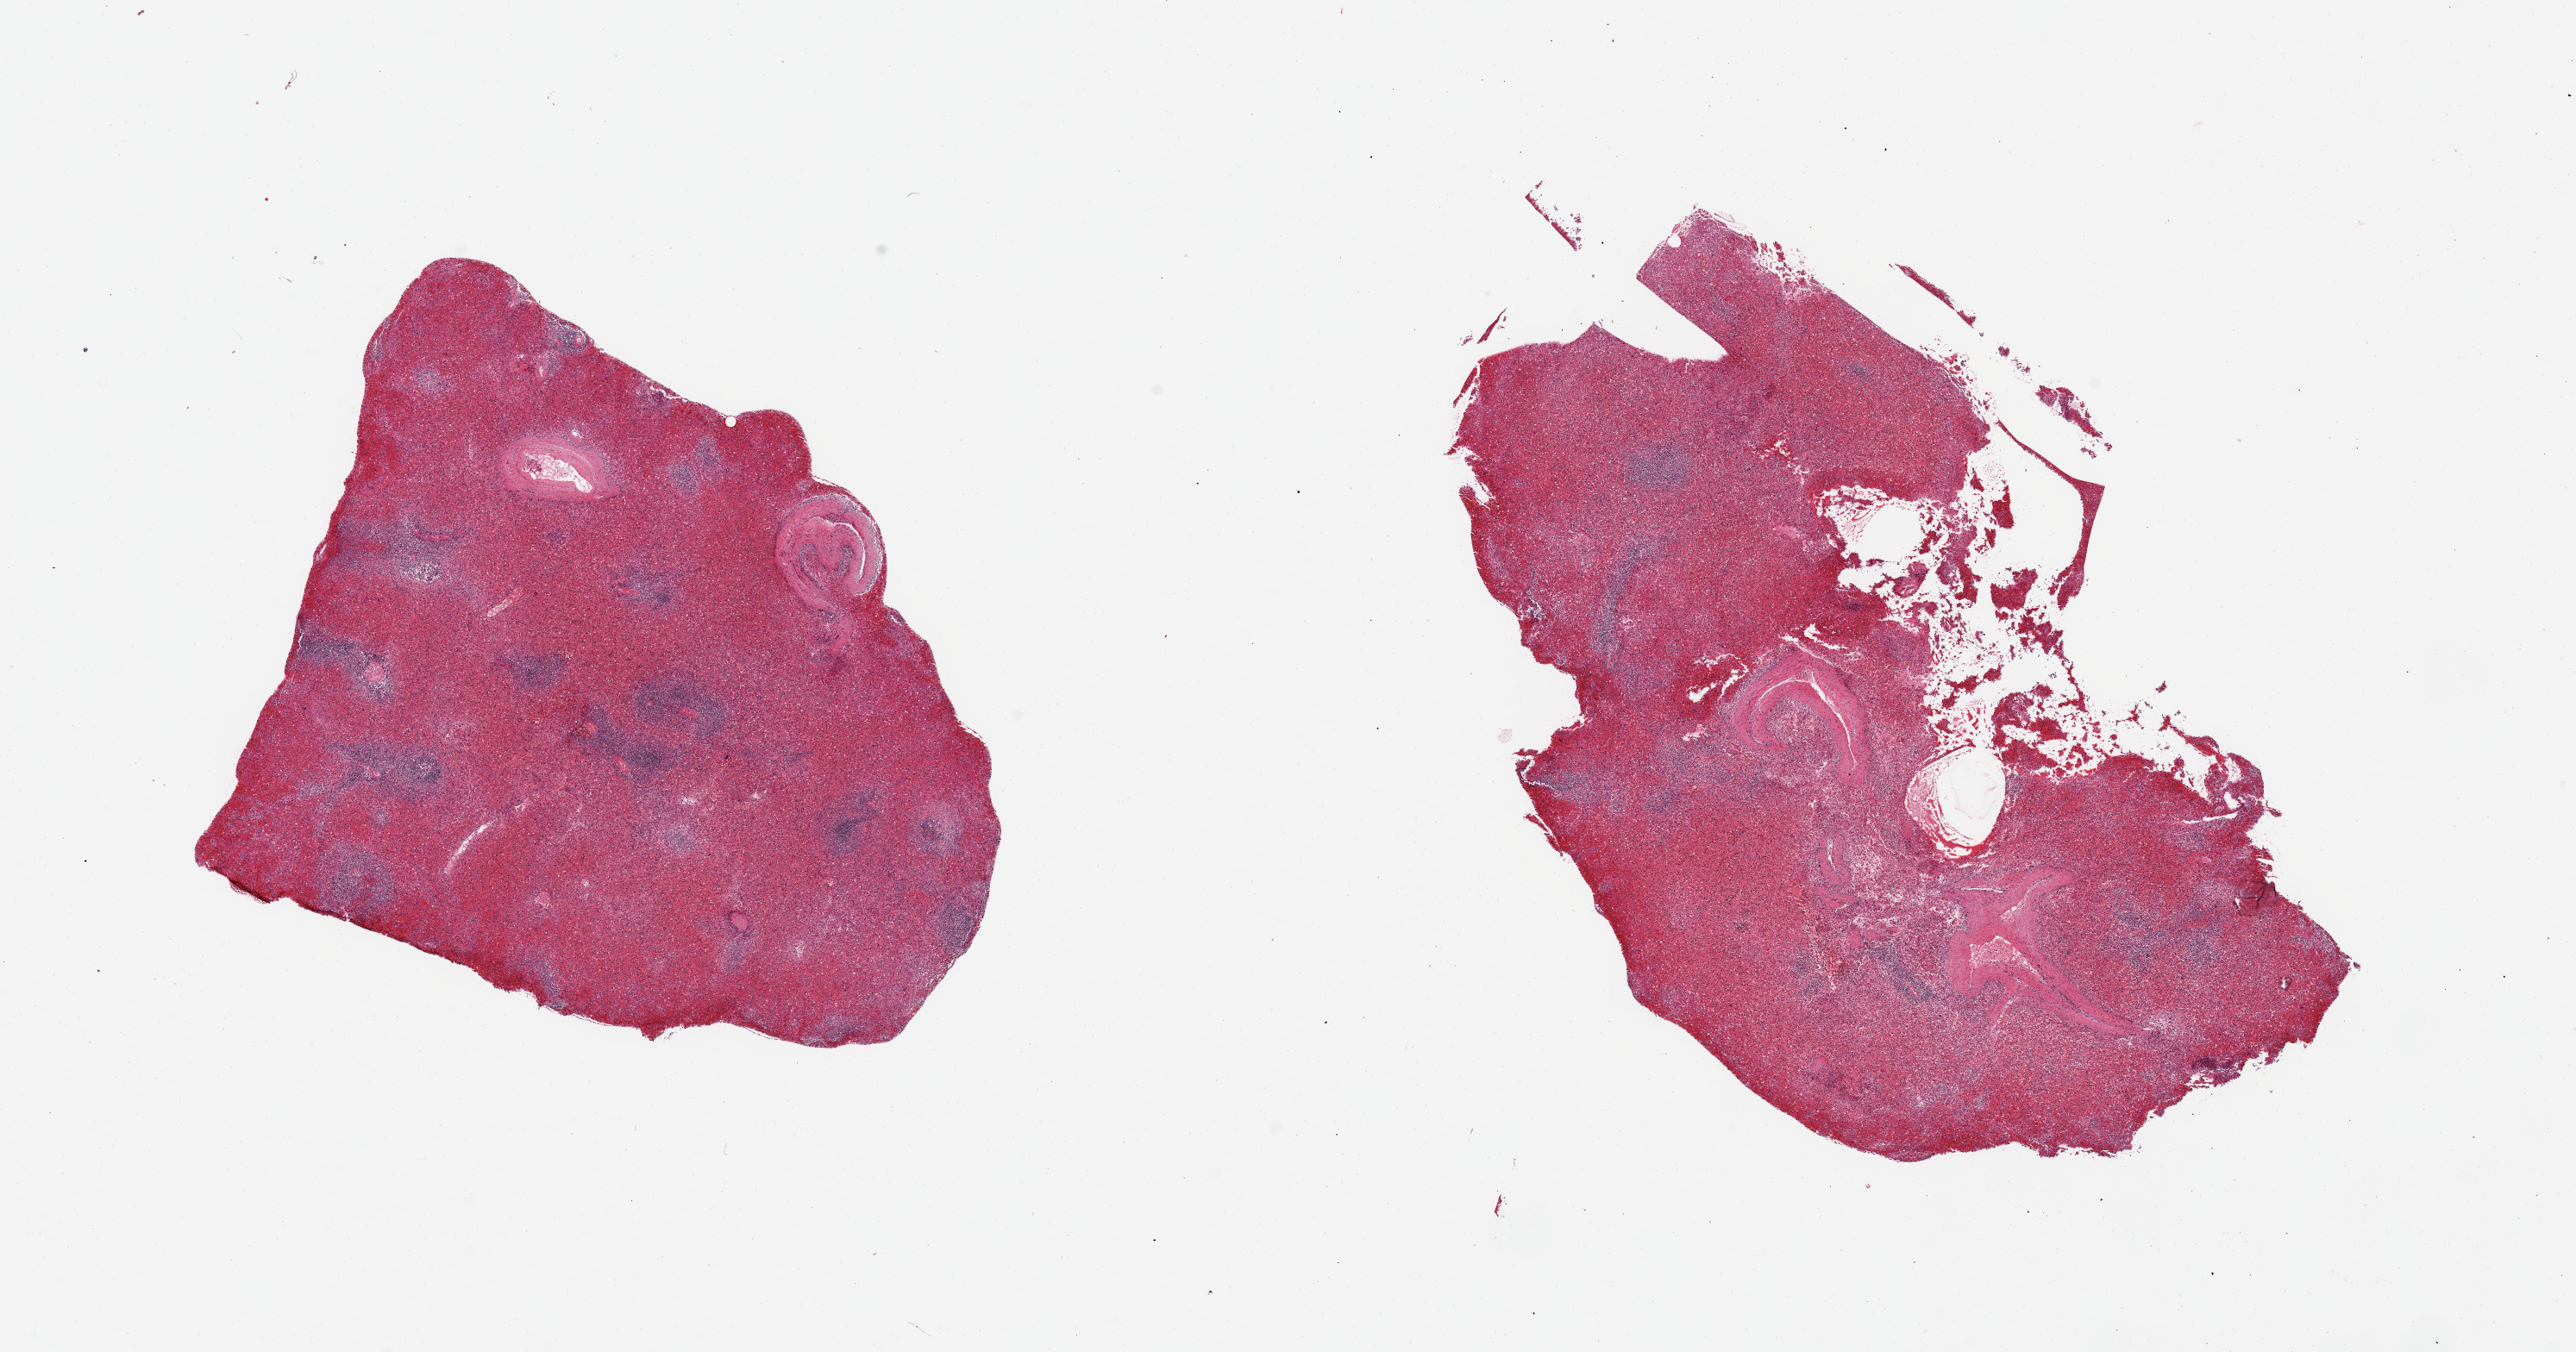
Whole-slide image, hematoxylin and eosin (H&E) stain, a low-resolution overview of the entire scanned area, about 23.6 x 12.4 mm, PAXgene-fixed, paraffin-embedded tissue, sampled site (target tissue): spleen, tissue donor sample. Donor sex: female.
Review note (as recorded): 2 pieces, congtested, autolyzed.